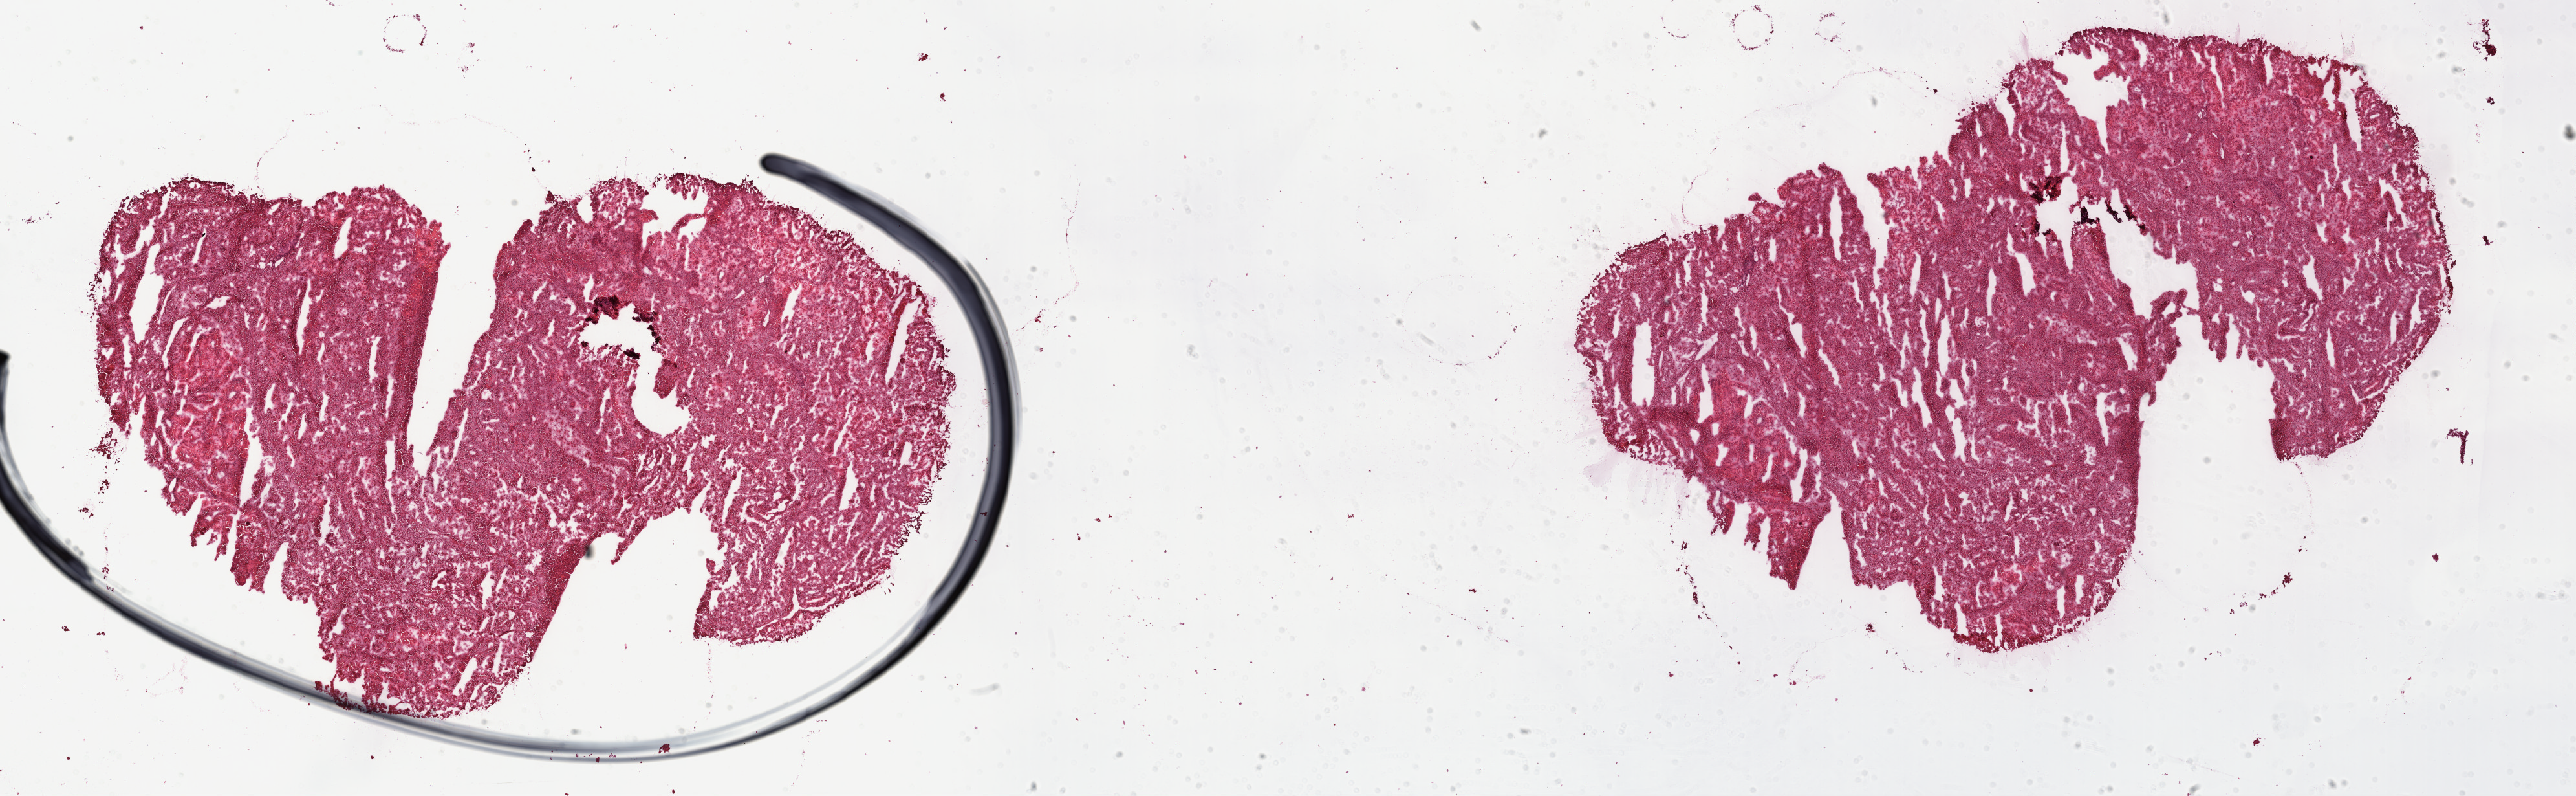
Digitized Hematoxylin and eosin (H&E) stained tissue section (whole slide), low-resolution overview of the scanned area, about 32.2 x 9.9 mm, frozen section, kidney, primary tumour sample. Male patient; age at initial diagnosis 59 years. Slide review estimates, as recorded: tumour cells 100%, tumour nuclei 75%, normal cells 0%, stromal cells 0%, necrosis 0%. Inflammatory infiltration, as recorded: lymphocyte infiltration 1%, monocyte infiltration 9%, neutrophil infiltration 0%.
Diagnosis: Papillary adenocarcinoma, NOS.